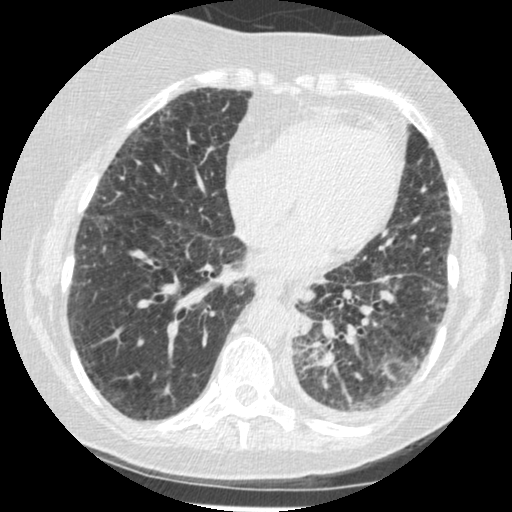
Low-dose screening chest CT, one axial slice; slice 73 of 341 in the series (ordered by position); lung window (W 1500 / L -600 HU); 1.25 mm slice thickness; 512 × 512 image matrix, field of view 310 × 310 mm.
Annotated regions visible in this slice (outlined manually by an expert reader):
- lesion 1 (tumor, lower lobe of left lung): bounding box <294,324,309,335> (left, top, right, bottom; pixels)